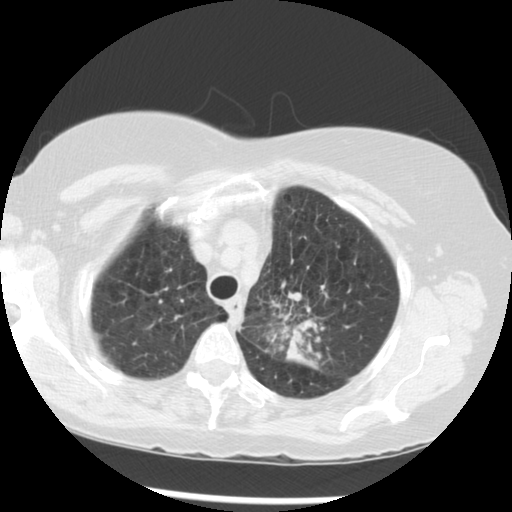
Axial slice from a low-dose chest CT screening exam. Third screening round (two years after baseline). Lung window (W 1500 / L -600 HU). Slice 230 of 283 in the series. 512 × 512 image matrix. Female participant, aged 70 years at enrolment.
Expert reader's lesion annotation, bounding box <255,280,352,369> (left, top, right, bottom; pixels). Screening reader's record for this exam (one nodule recorded; not confirmed to be the boxed lesion): non-calcified nodule or mass ≥4 mm, left upper lobe, 32 × 26 mm, spiculated (stellate) margins, soft tissue attenuation, pre-existing on the prior screen: yes; interval growth: yes. Official screen result: positive, other. Lung cancer was diagnosed 24 days after this screen: neoplasm, malignant, left upper lobe, stage IIIB (AJCC 6th edition), 40 mm at pathology.